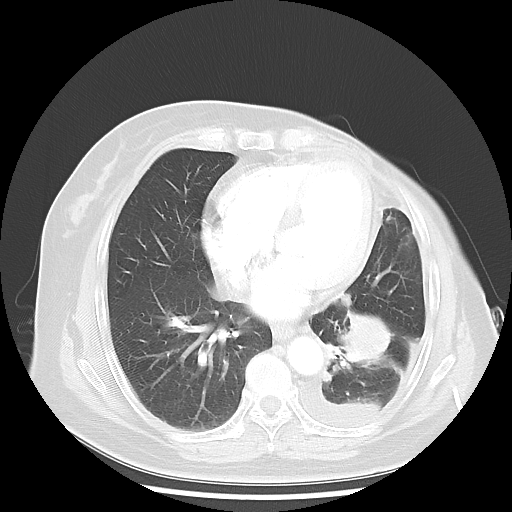
Chest CT, one axial slice; slice 17 of 48 in the series (ordered by position); reconstruction kernel LUNG; lung window (W 1500 / L -600 HU); 5 mm slice thickness; 512 × 512 image matrix, field of view 360 × 360 mm. Patient: female, 63 years. Case-level facts recorded for this patient, not image findings: clinical TNM (as recorded): T2 N0 M1.
Annotated regions visible in this slice (rectangle marked by the reading radiologist):
- lung tumour (recorded histology: adenocarcinoma): bounding box [x1, y1, x2, y2] px = [332, 313, 395, 370]